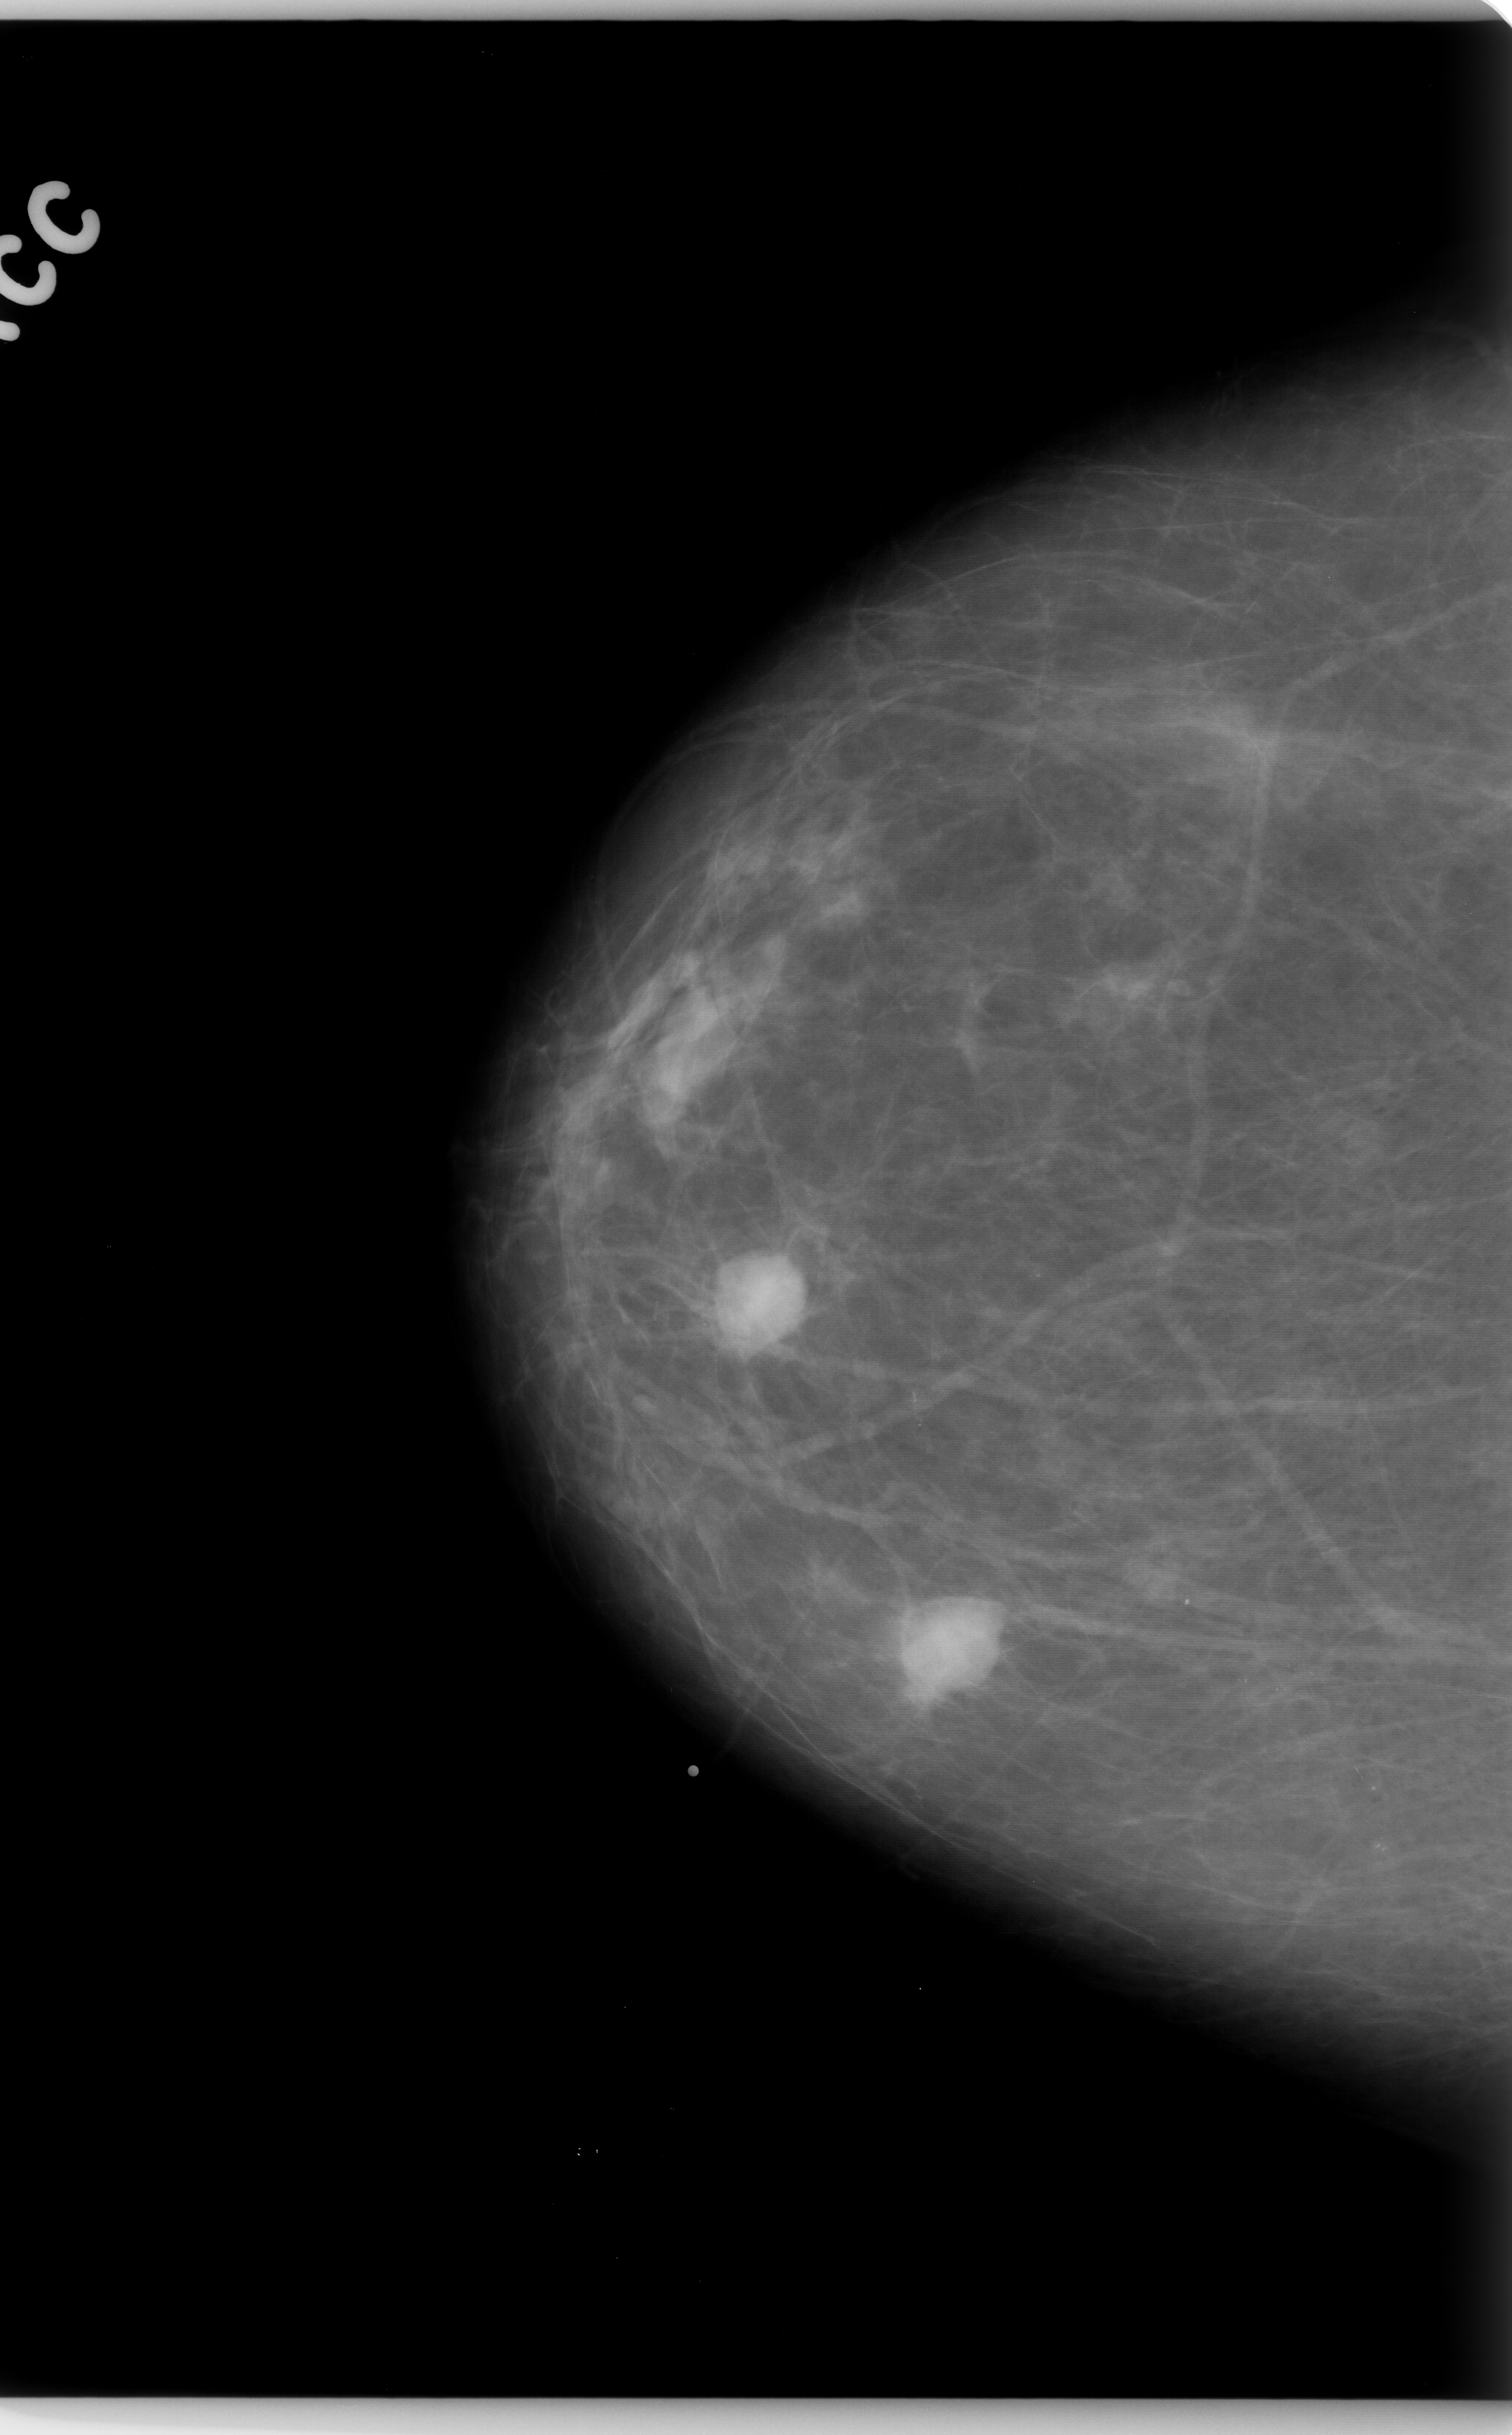
Mammogram (digitized film). Right breast. Craniocaudal (CC) view. BI-RADS breast density category 1 (scale 1–4). 1512 × 2435 image matrix.
Marked abnormalities (boxes around the expert regions of interest):
- Finding 1 of 3: mass, shape oval, margins circumscribed; BI-RADS assessment category 4; subtlety rating 5 on a 1 (subtle) to 5 (obvious) scale; pathology (as recorded): benign: bounding box <619,984,737,1132> (left, top, right, bottom; pixels)
- Finding 2 of 3: mass, shape oval, margins microlobulated; BI-RADS assessment category 4; pathology (as recorded): malignant: <700,1246,810,1359>
- Finding 3 of 3: mass, shape oval, margins microlobulated; BI-RADS assessment category 4; subtlety rating 5 on a 1 (subtle) to 5 (obvious) scale; pathology (as recorded): malignant: <875,1584,1014,1715>